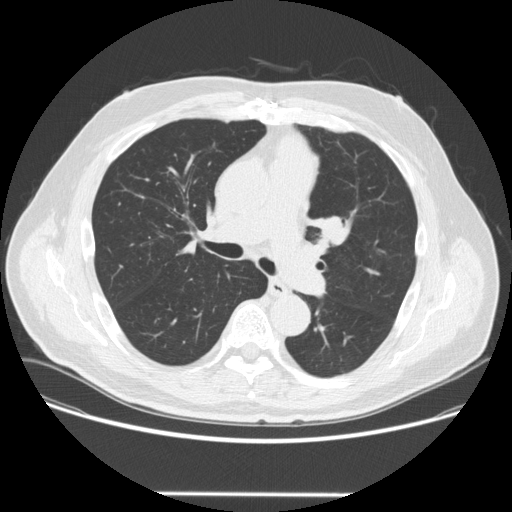
Axial slice from a low-dose chest CT screening exam, third screening round (two years after baseline), lung window (W 1500 / L -600 HU), 2.5 mm slice thickness, 120 kVp, slice 92 of 253 in the series. Male, age 66 years at enrolment.
Expert-annotated lung lesion, box from (x=307, y=206) to (x=359, y=254) px. The screening reader recorded 2 non-calcified nodules or masses ≥4 mm on this exam (left upper lobe, right lower lobe); which of them this box marks is not recorded. Participant outcome: lung cancer diagnosed 85 days after this screen — squamous cell carcinoma, NOS, left upper lobe, poorly differentiated (G3), stage IA (AJCC 6th edition), 27 mm at pathology.